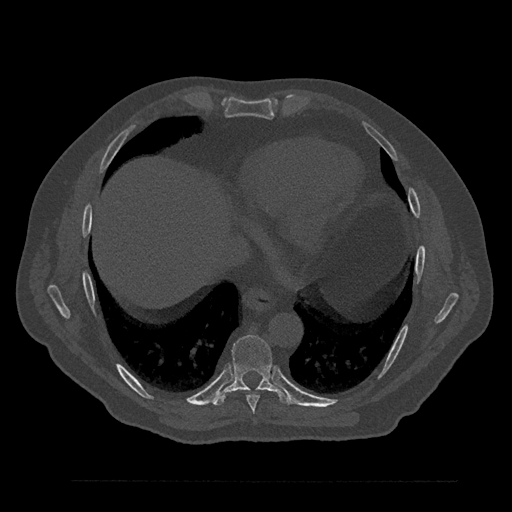
CT including the spine, one axial slice; position 426 of 797 along the scan axis; reconstruction kernel Br40s/3; 120 kVp; bone window (W 1800 / L 400 HU); 512 × 512 image matrix. Male patient, age 61 years. From the clinical record (not read from this slice): primary cancer: prostate.
Annotated regions visible in this slice (semi-automatic segmentation, software-assisted and operator-edited):
- T8 vertebra: bounding box <240,390,260,413> (left, top, right, bottom; pixels)
- T9 vertebra: <214,335,292,406>